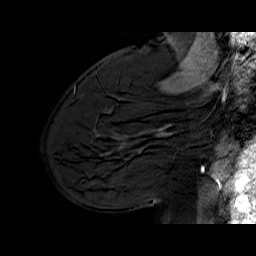
Breast MRI (dynamic contrast-enhanced), one sagittal slice; slice 45 of 70 in the series (ordered by position); dynamic contrast-enhanced series, time point 2 of 6 at this slice position (early post-contrast); 1.5 T; TE 6.5 ms, TR 33 ms; 256 × 256 image matrix, field of view 200 × 200 mm. Female patient. From the clinical record (not read from this slice): setting: breast cancer imaged before/during neoadjuvant chemotherapy; receptor status: HER2-positive.
Annotated regions visible in this slice (semi-automatic segmentation, software-assisted and operator-edited):
- analysis volume of interest (the breast-tissue region the enhancement analysis was run in; not a lesion): box from (x=113, y=112) to (x=174, y=170) px
- tumour enhancement mask (voxels above the 100 % enhancement threshold inside the analysis volume of interest): (x=157, y=124)–(x=172, y=135)